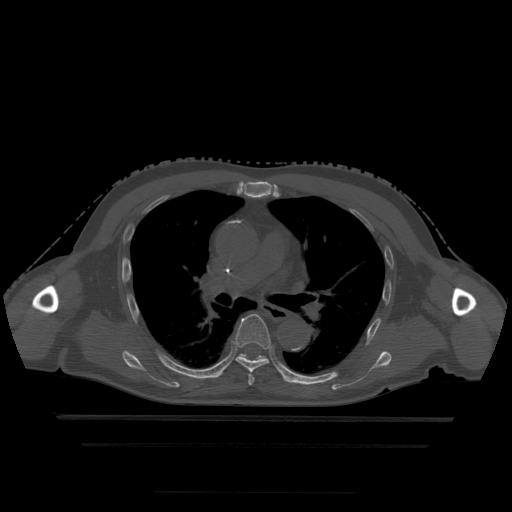
CT including the spine, one axial slice; slice 316 of 522 in the series (ordered by position); bone window (W 1800 / L 400 HU); 512 × 512 image matrix, field of view 436 × 436 mm. Patient age 68 years. Case-level facts recorded for this patient, not image findings: primary cancer: urothelial.
Outlined on this slice (semi-automatic segmentation, software-assisted and operator-edited):
- T5 vertebra: bounding box <248,375,255,386> (left, top, right, bottom; pixels)
- T6 vertebra: <235,314,273,373>
- T7 vertebra: <240,354,266,360>